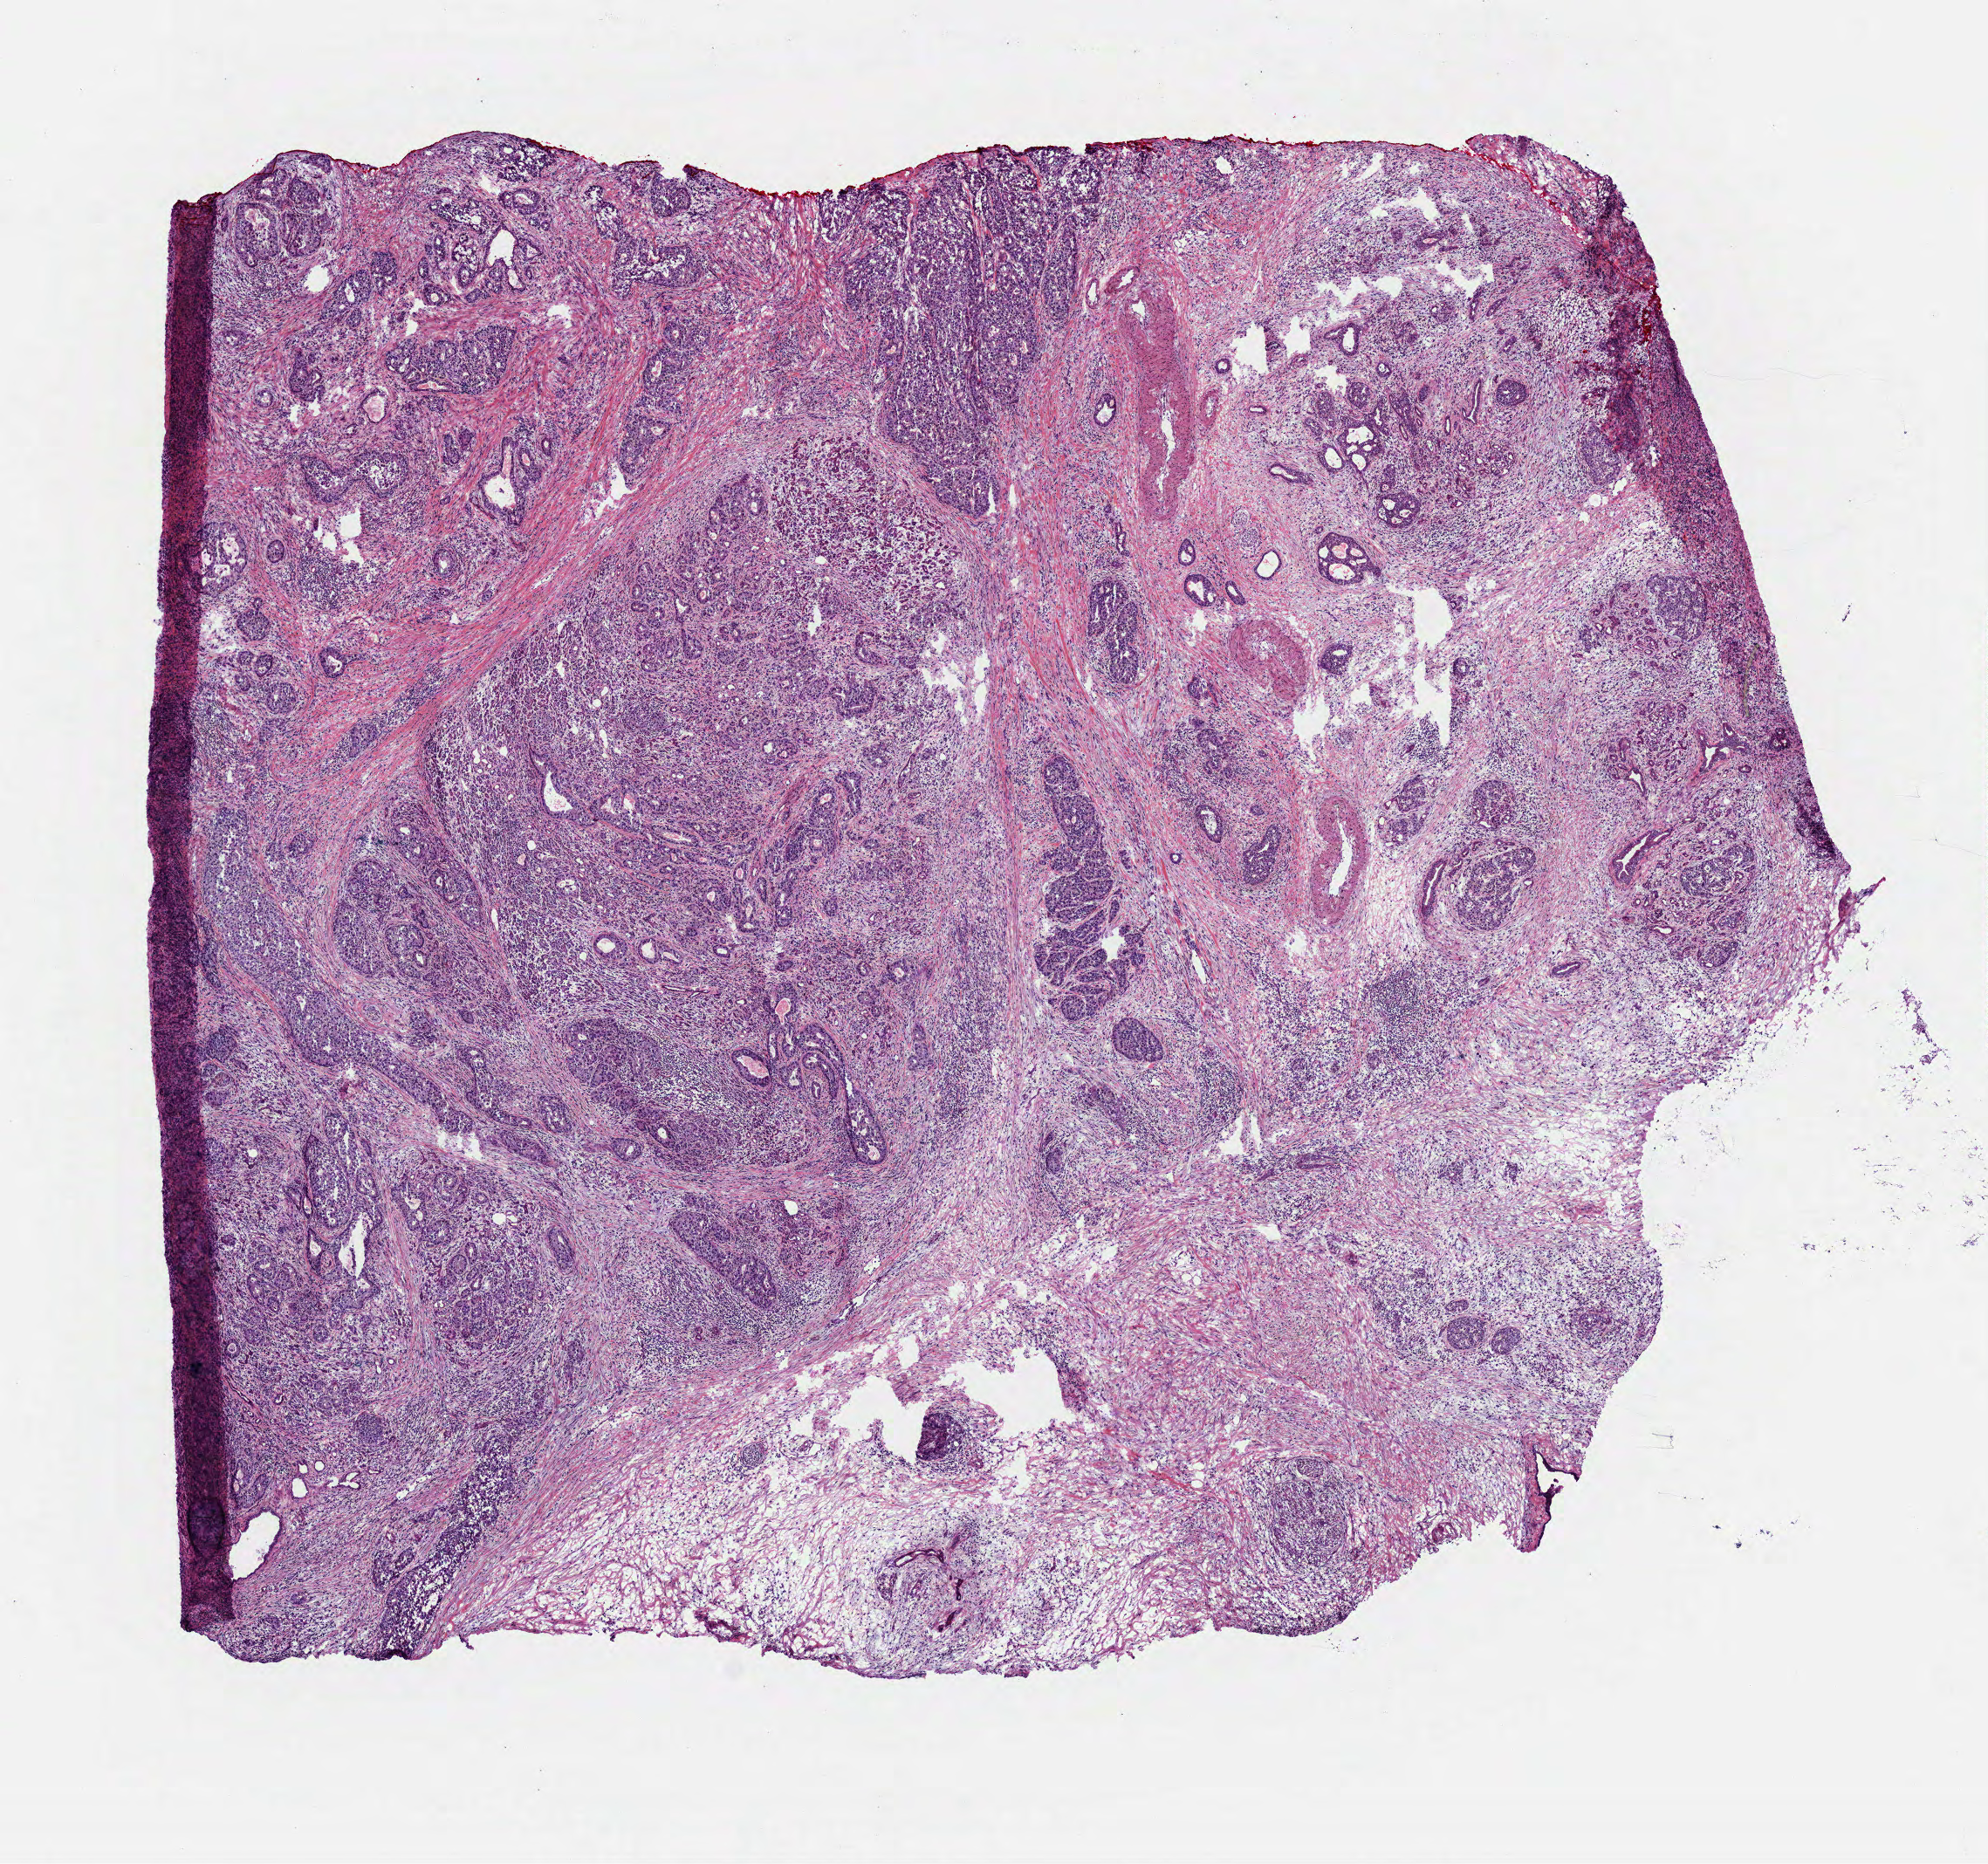
Digitized Hematoxylin and eosin (H&E) stained tissue section (whole slide) — a low-resolution overview of the entire scanned area, about 9.2 x 8.6 mm (slide scanned at 40x). Frozen section. Primary tumour sample from the pancreas. Male patient; age at initial diagnosis 72 years.
Diagnosis: Infiltrating duct carcinoma, NOS (head of pancreas).